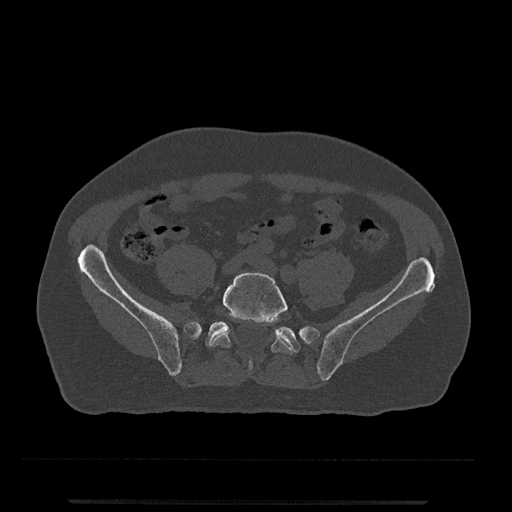
CT including the spine, one axial slice; slice 52 of 797 in the series (ordered by position); reconstruction kernel Br40s/3; 120 kVp; bone window (W 1800 / L 400 HU); 512 × 512 image matrix. Patient: male, 63 years. Case-level facts recorded for this patient, not image findings: primary cancer: prostate.
Outlined on this slice (semi-automatically segmented with operator editing):
- L5 vertebra: box from (x=210, y=272) to (x=292, y=371) px